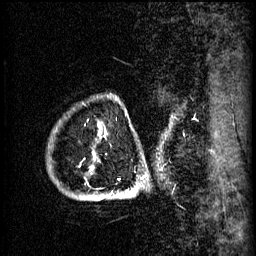
Breast MRI (dynamic contrast-enhanced), one sagittal slice; slice 57 of 60 in the series (ordered by position); 3 images stored at this slice position (order not interpretable as contrast timing); 1.5 T; TE 4.2 ms, TR 11 ms; 256 × 256 image matrix. Female patient, age 51 years.
Structures marked on this image (semi-automatic segmentation, software-assisted and operator-edited):
- analysis volume of interest (the breast-tissue region the enhancement analysis was run in; not a lesion): bounding box <57,98,147,197> (left, top, right, bottom; pixels)
- tumour enhancement mask (voxels above the 70 % enhancement threshold inside the analysis volume of interest): <105,136,121,181>